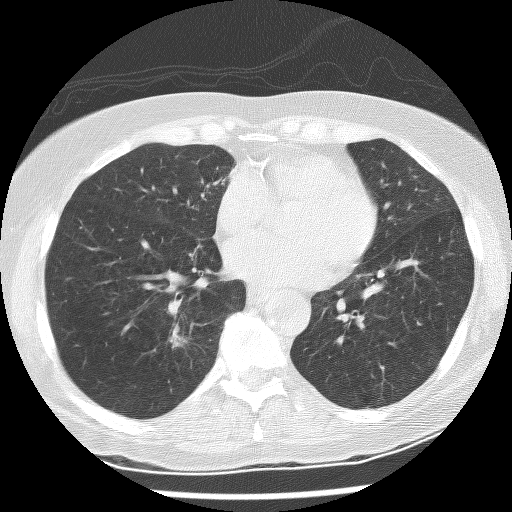
Low-dose screening chest CT, axial slice; first (baseline) screen; lung window (W 1500 / L -600 HU); 2.5 mm slice thickness; lung (sharp) reconstruction kernel (BONE); slice 145 of 247 in the series. Female, age 60 years at enrolment. Former smoker at enrolment.
• Expert-annotated lung lesion, bounding box [x1, y1, x2, y2] px = [155, 322, 203, 357].
• Reader record for this screening exam (exam-level; its link to the box is not recorded): non-calcified nodule or mass ≥4 mm, right lower lobe, 10 × 6 mm, spiculated (stellate) margins, mixed attenuation.